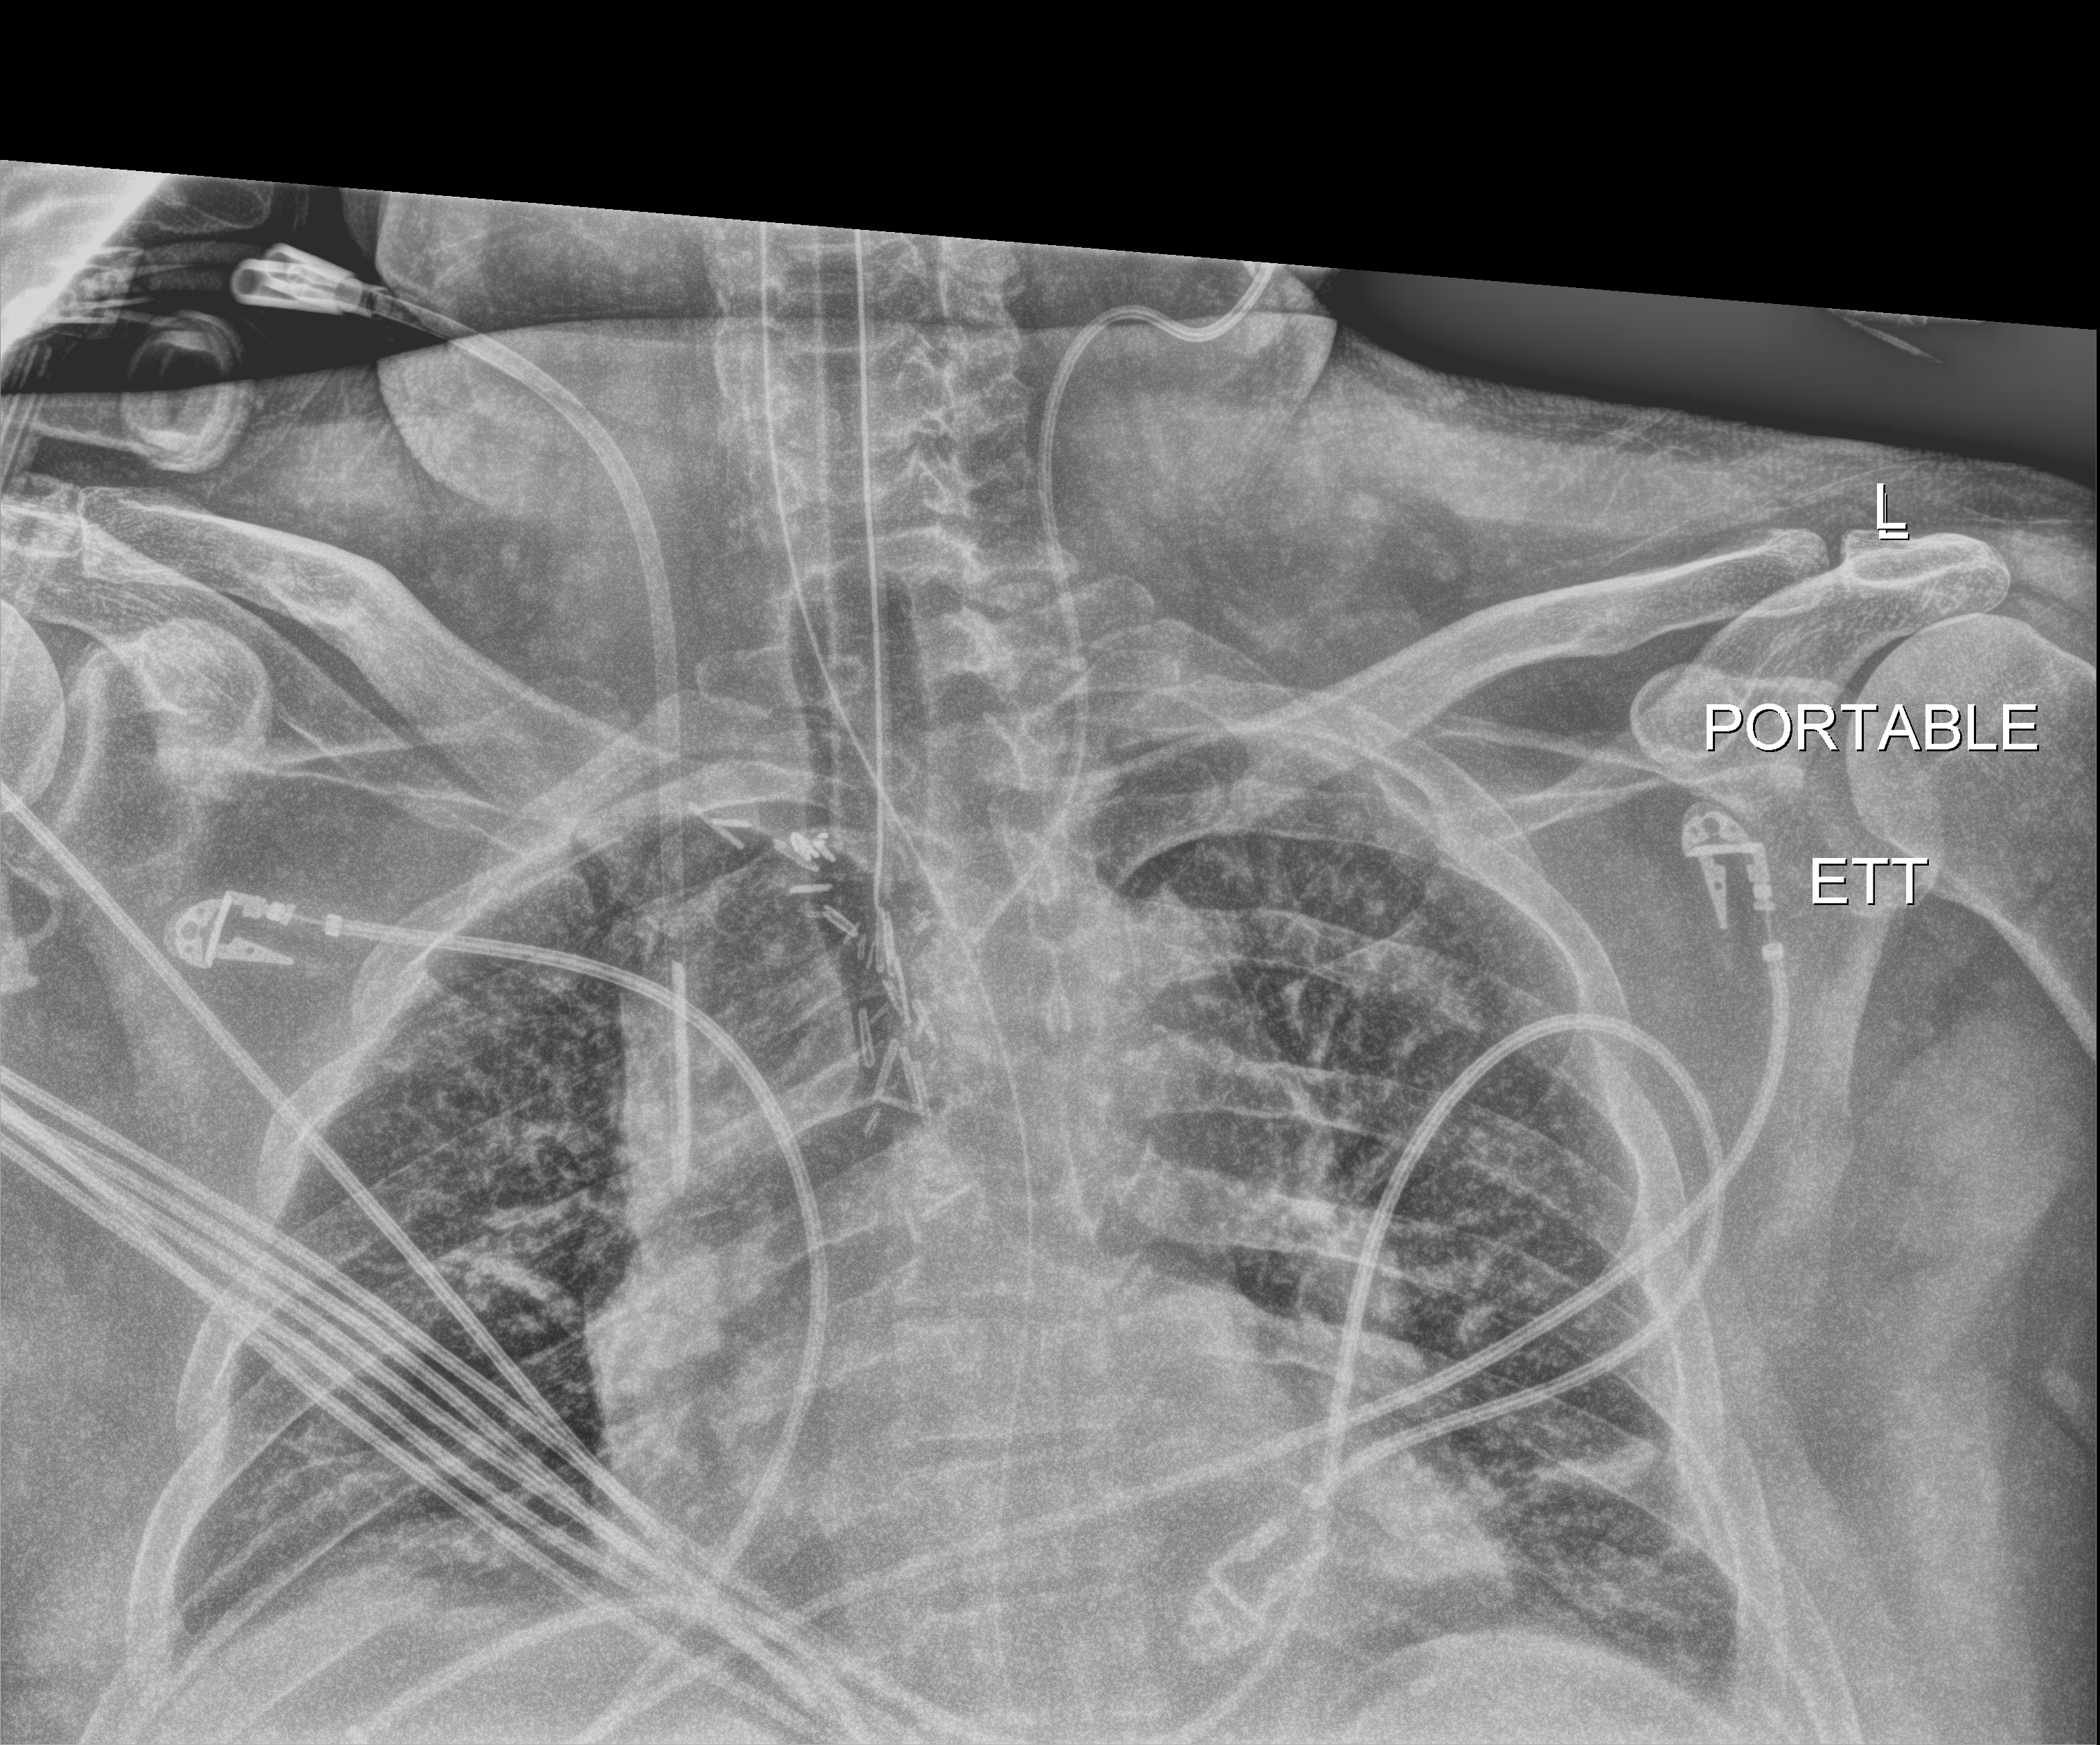
Chest X-ray (portable), anteroposterior (AP) projection. Patient hospitalised with COVID-19, aged 18–59 years.
From the hospital-stay record, not from the radiograph (when in the stay this image was taken is not recorded): mechanically ventilated during this hospital stay: yes.